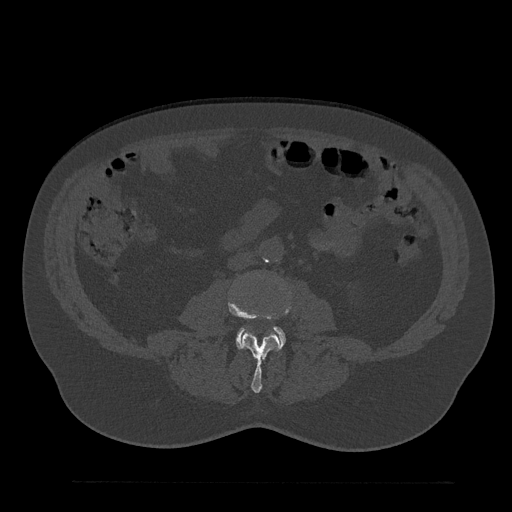
CT including the spine, one axial slice. Position 7 of 797 along the scan axis. Reconstruction kernel Br40s/3. Bone window (W 1800 / L 400 HU). 0.5 mm slice thickness. 512 × 512 image matrix, field of view 430 × 430 mm. Patient: male, 61 years. Case-level facts recorded for this patient, not image findings: primary cancer: prostate.
Structures marked on this image (semi-automatically segmented with operator editing):
- L3 vertebra: bounding box (x1, y1, x2, y2) in pixels: (228, 296, 292, 393)
- L4 vertebra: (236, 327, 285, 348)